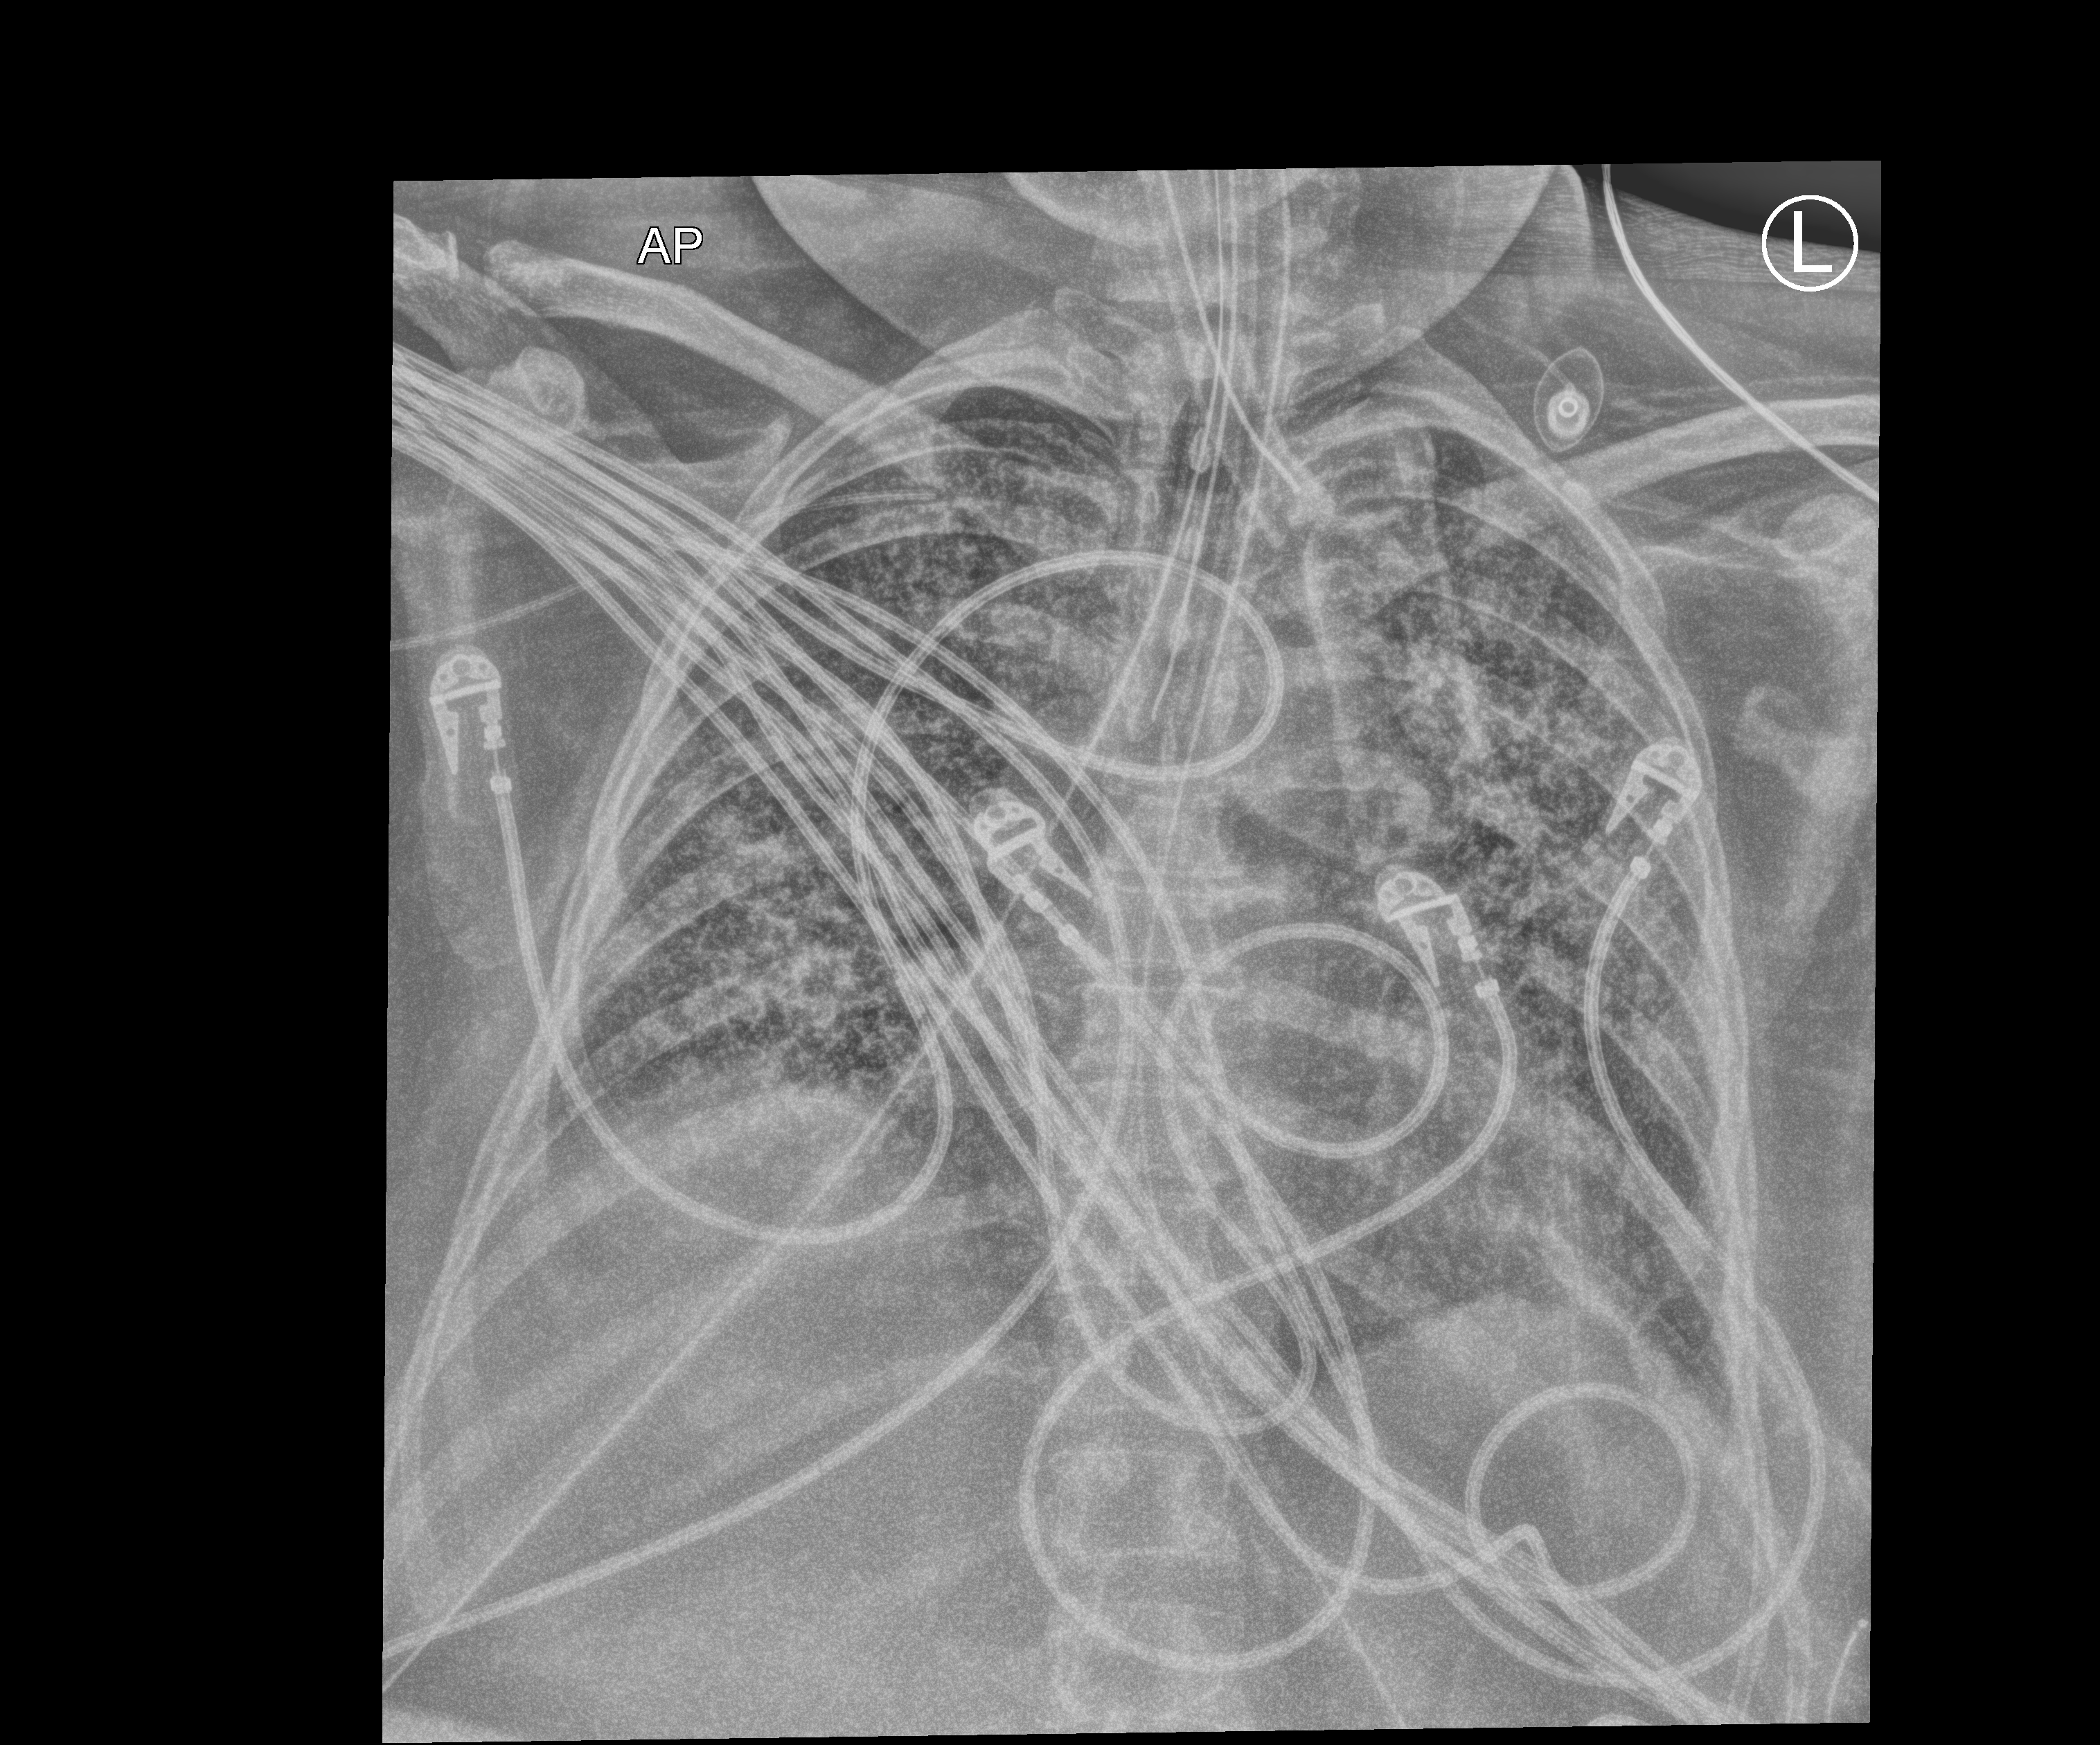
Bedside chest radiograph (computed radiography); anteroposterior (AP) projection. Patient hospitalised with COVID-19; female, aged 18–59 years.
Admission-level facts for this patient (not findings on this image; timing relative to this image not recorded):
- mechanically ventilated during this hospital stay: yes
- COPD (admission record): no